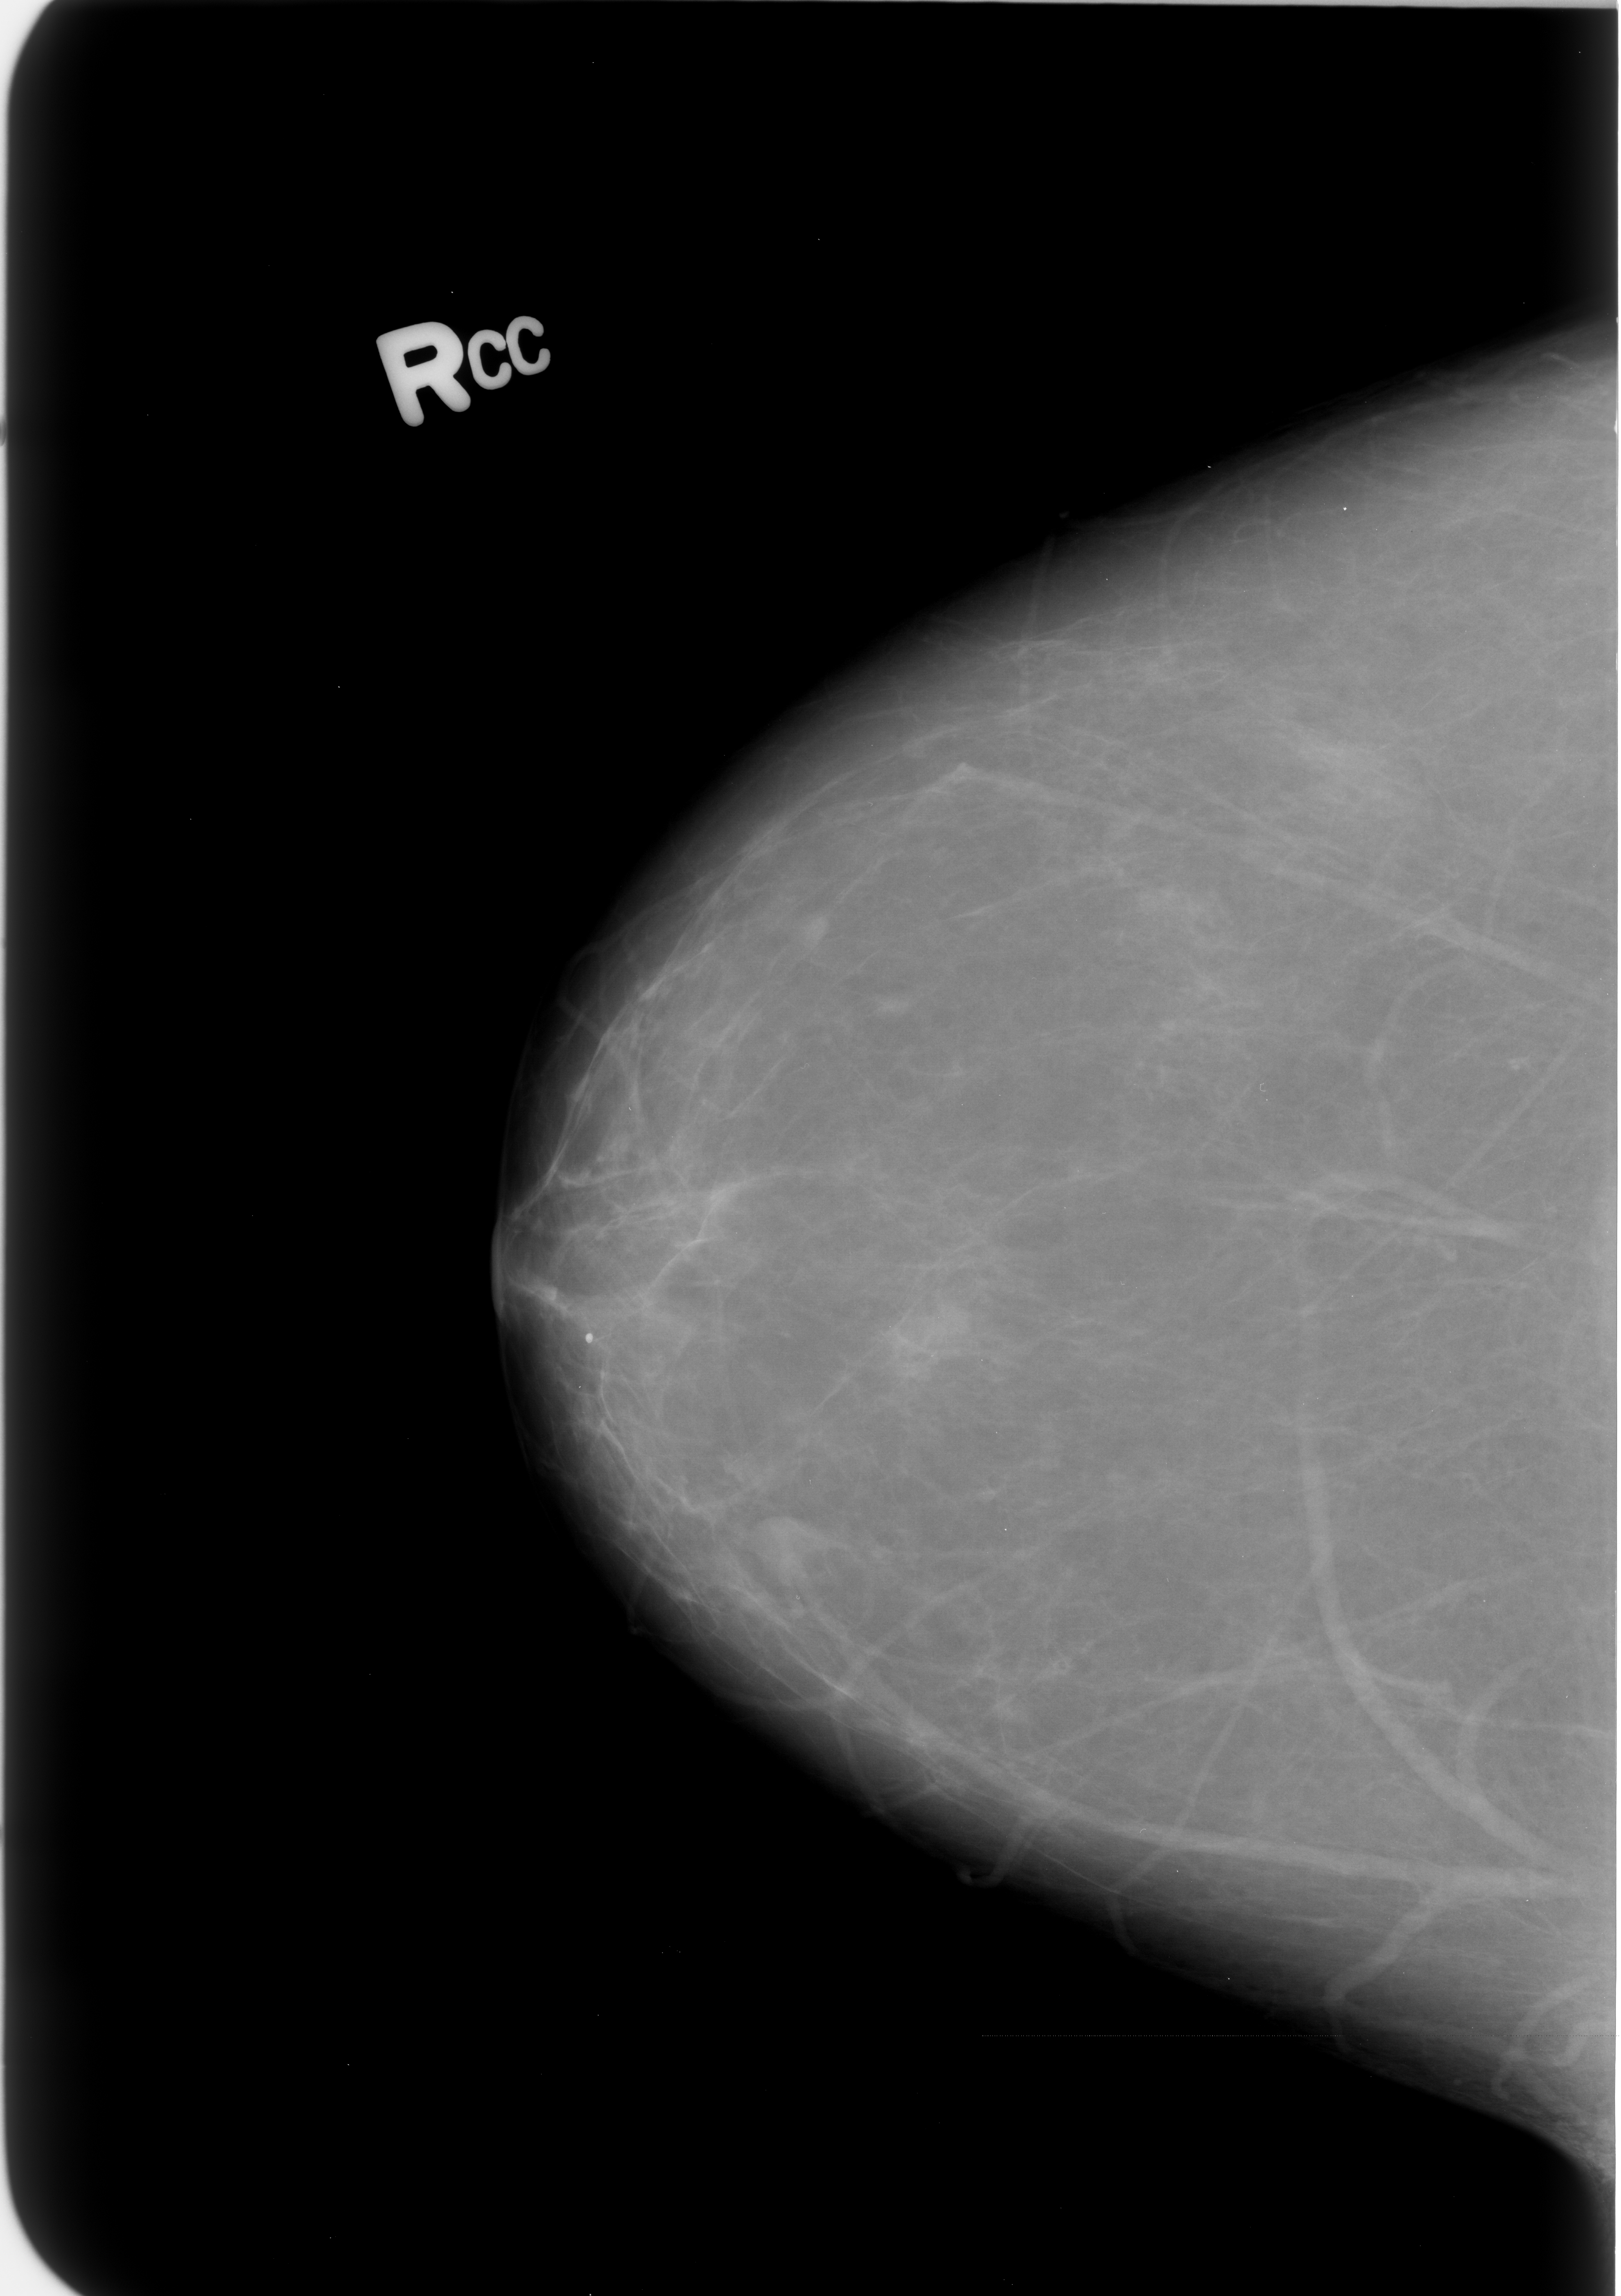
Scanned film-screen mammogram; right breast; craniocaudal (CC) view.
- Mass, shape lobulated, margins circumscribed / ill defined; BI-RADS assessment category 4; subtlety rating 3 on a 1 (subtle) to 5 (obvious) scale; pathology result (as recorded, not read from the image): benign.